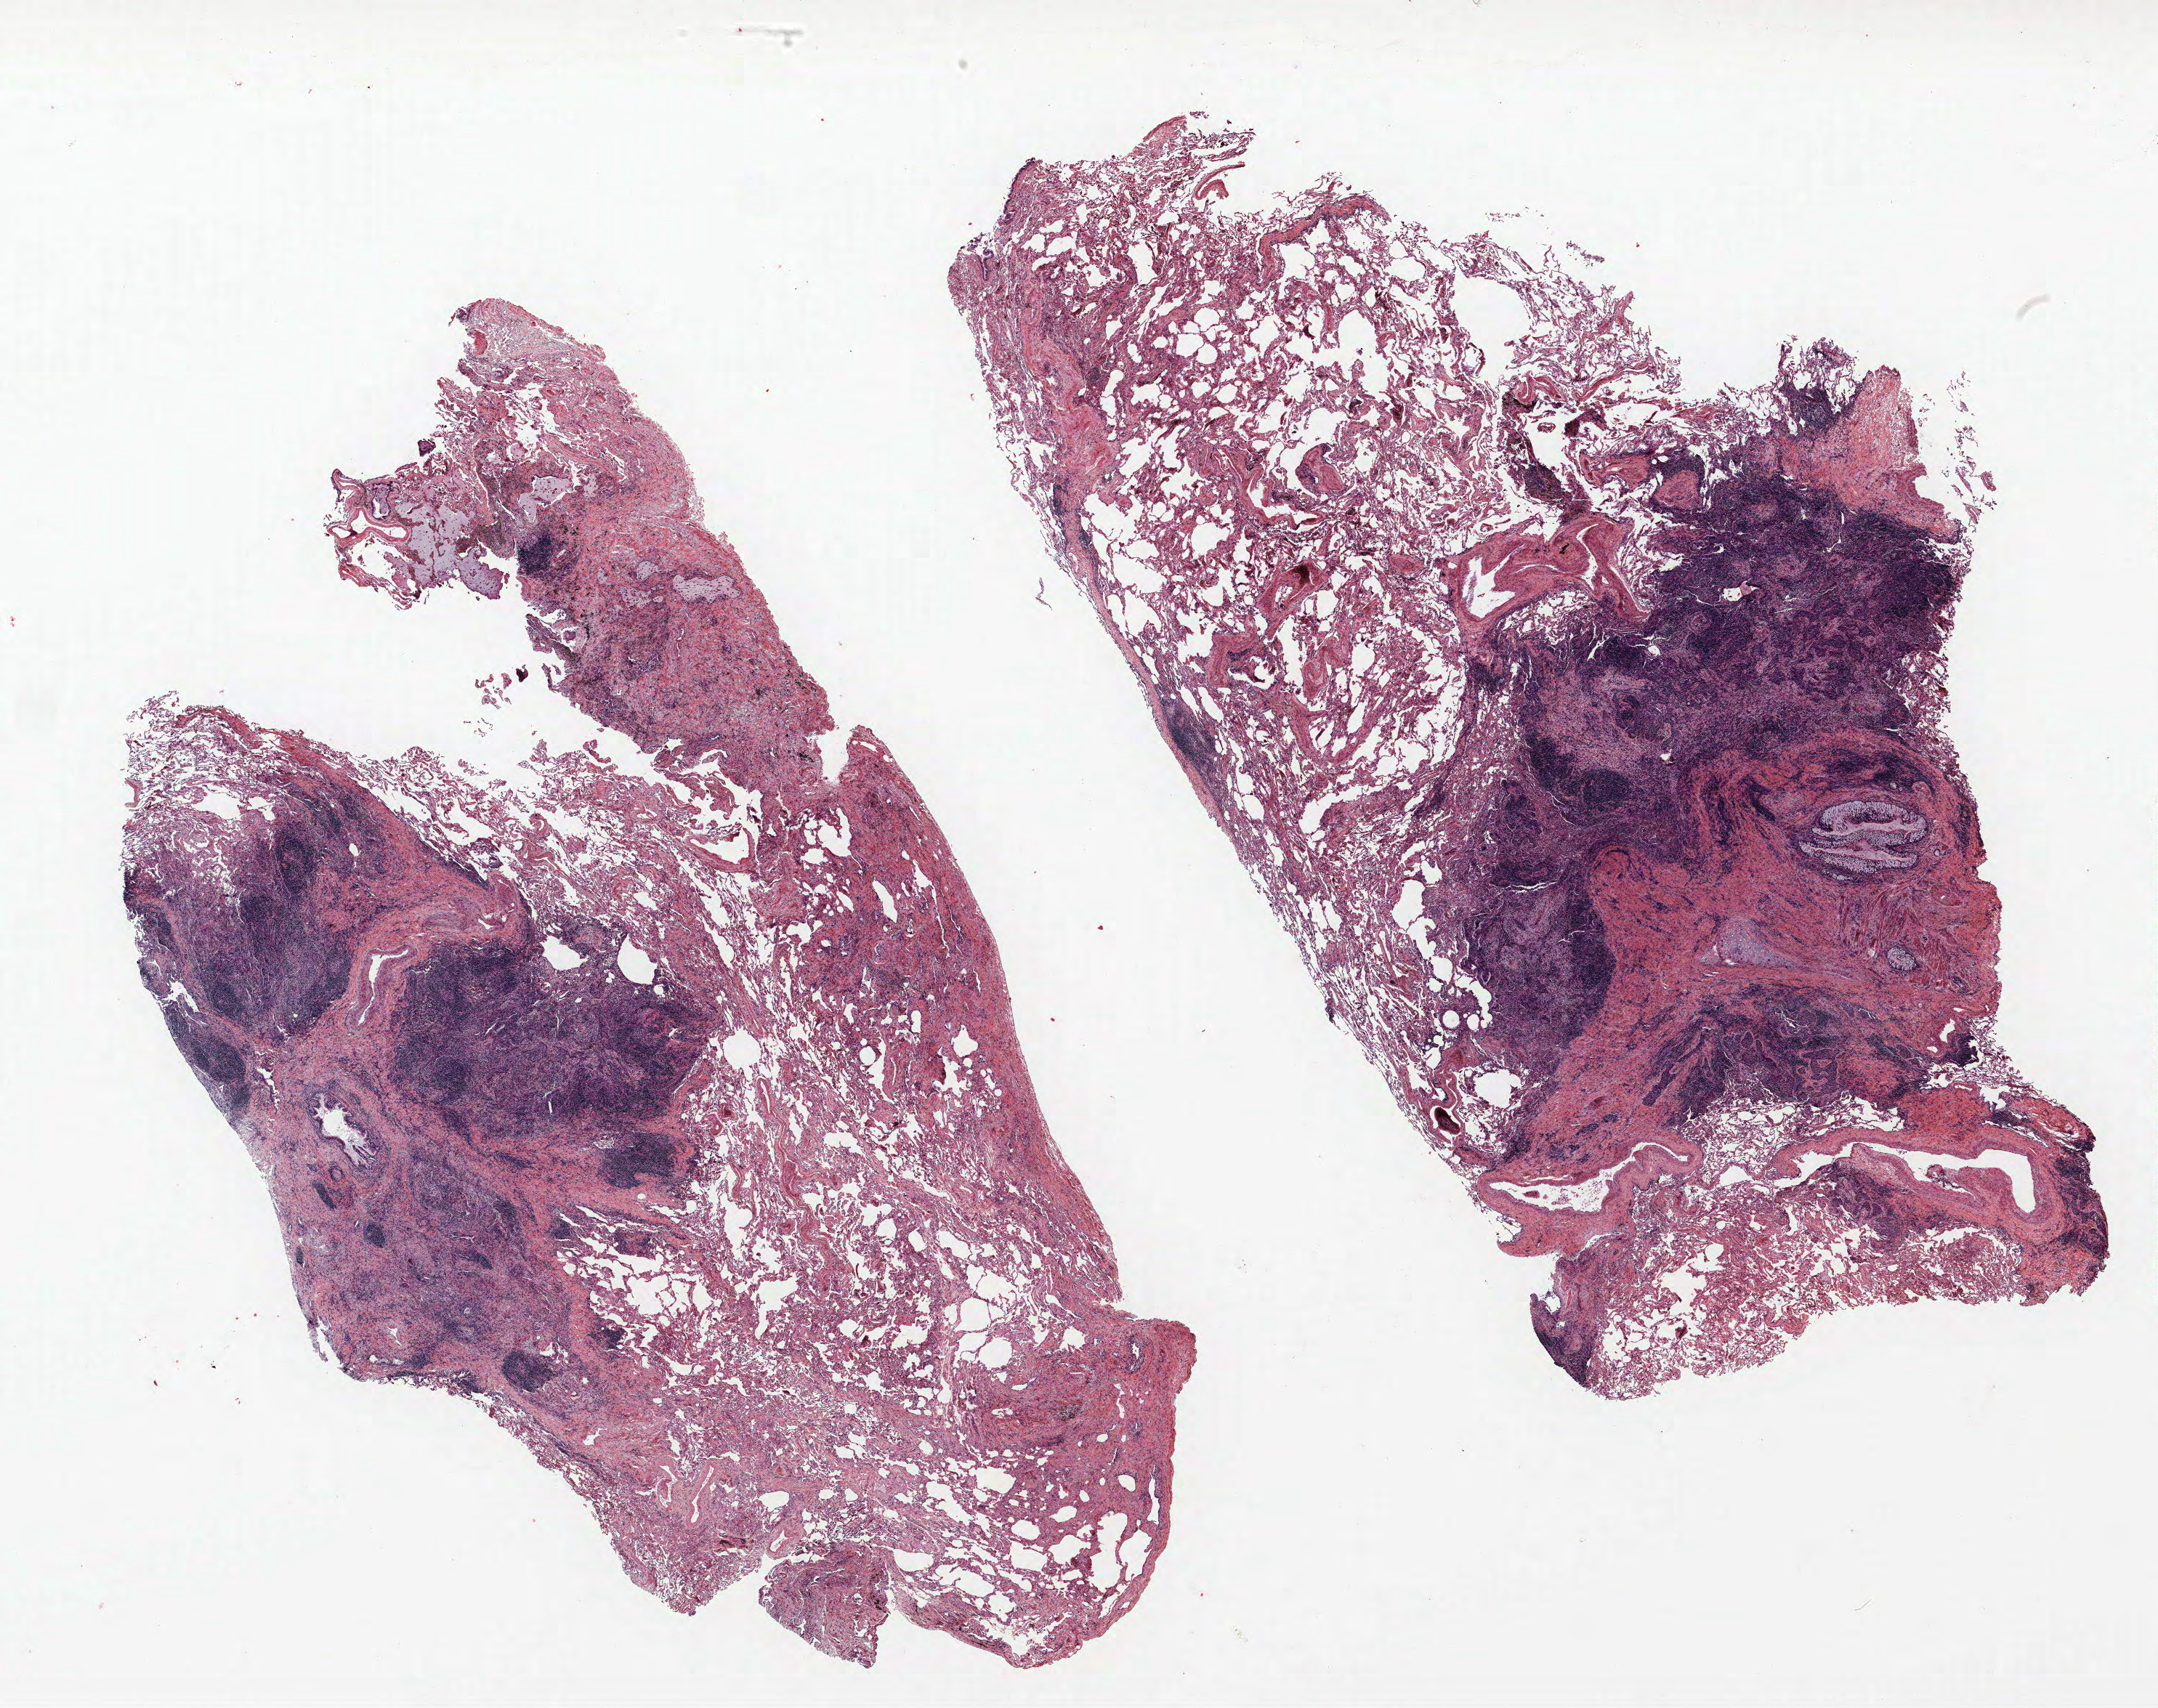
H&E whole-slide image, a low-resolution overview of the entire scanned area, about 23.8 x 18.8 mm, FFPE section, lung. Male patient, aged 68 at enrolment. Current smoker at enrolment.
Participant's lung-cancer diagnosis: Squamous cell carcinoma, NOS.